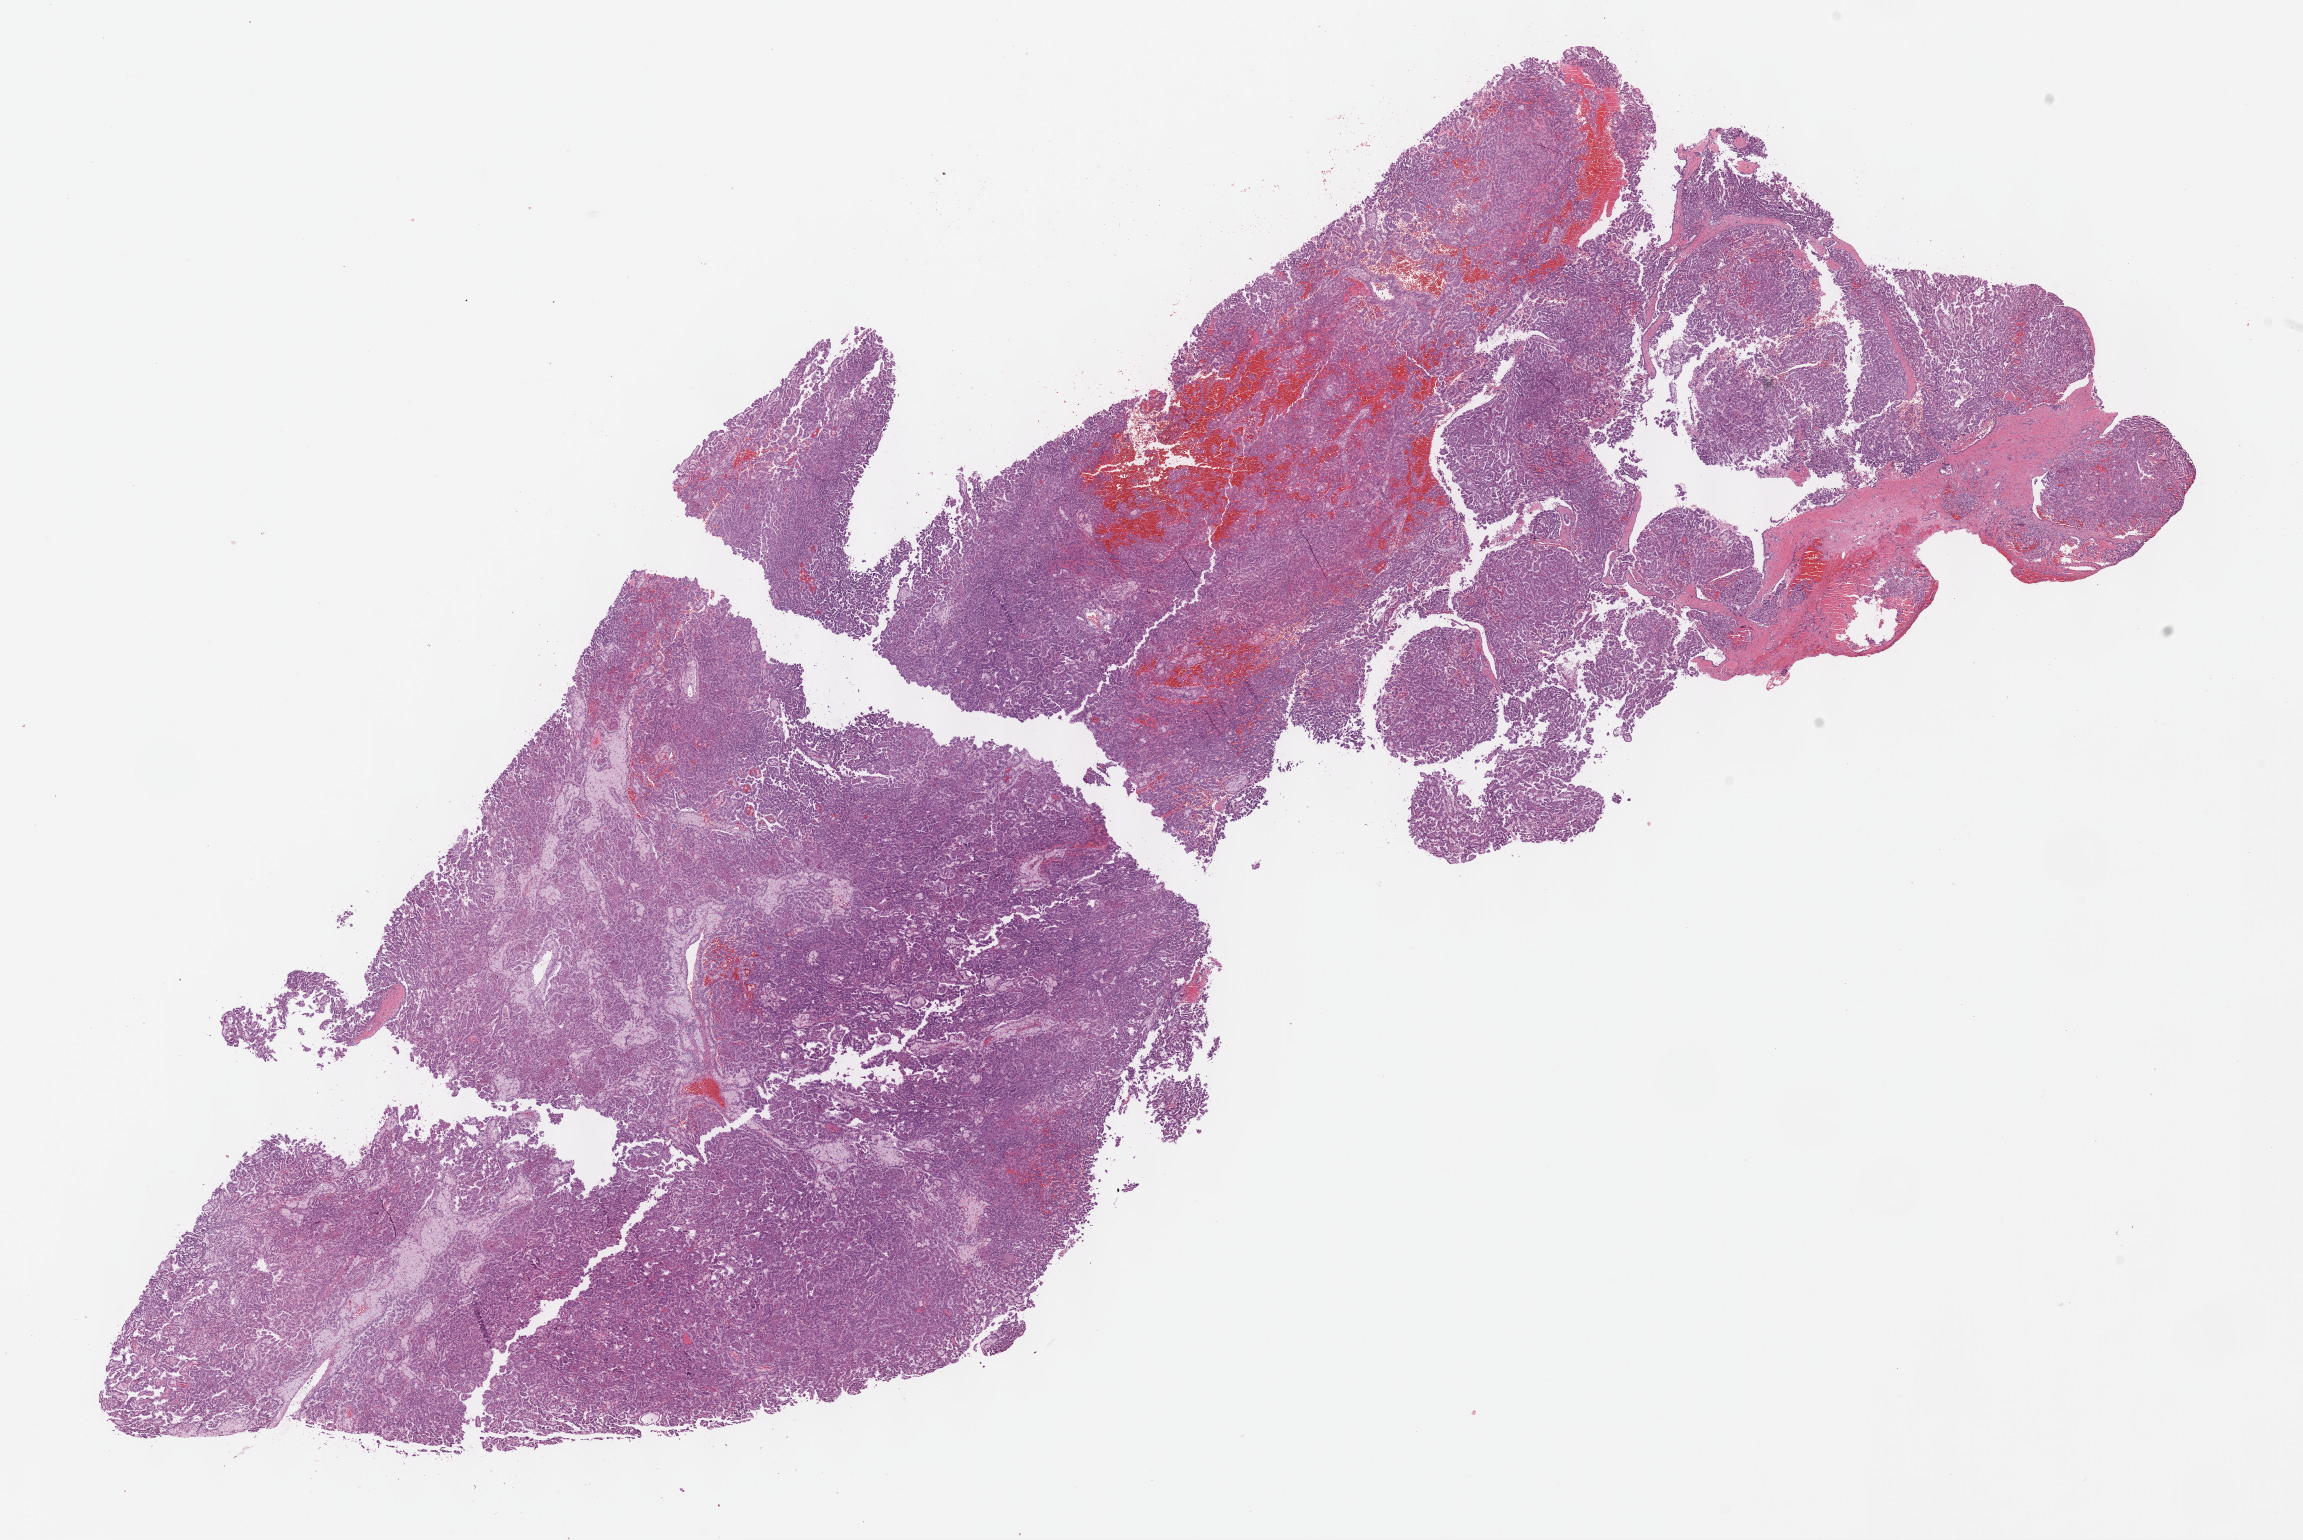
Digitized H&E tissue section (whole slide), low-resolution overview of the scanned area, about 18.6 x 12.5 mm; formalin-fixed paraffin-embedded (FFPE) diagnostic section; primary tumour sample from the kidney. Male patient; age at initial diagnosis 52 years.
Pathologic diagnosis: Papillary adenocarcinoma, NOS. Laterality: left. AJCC pathologic stage: I (7th edition).